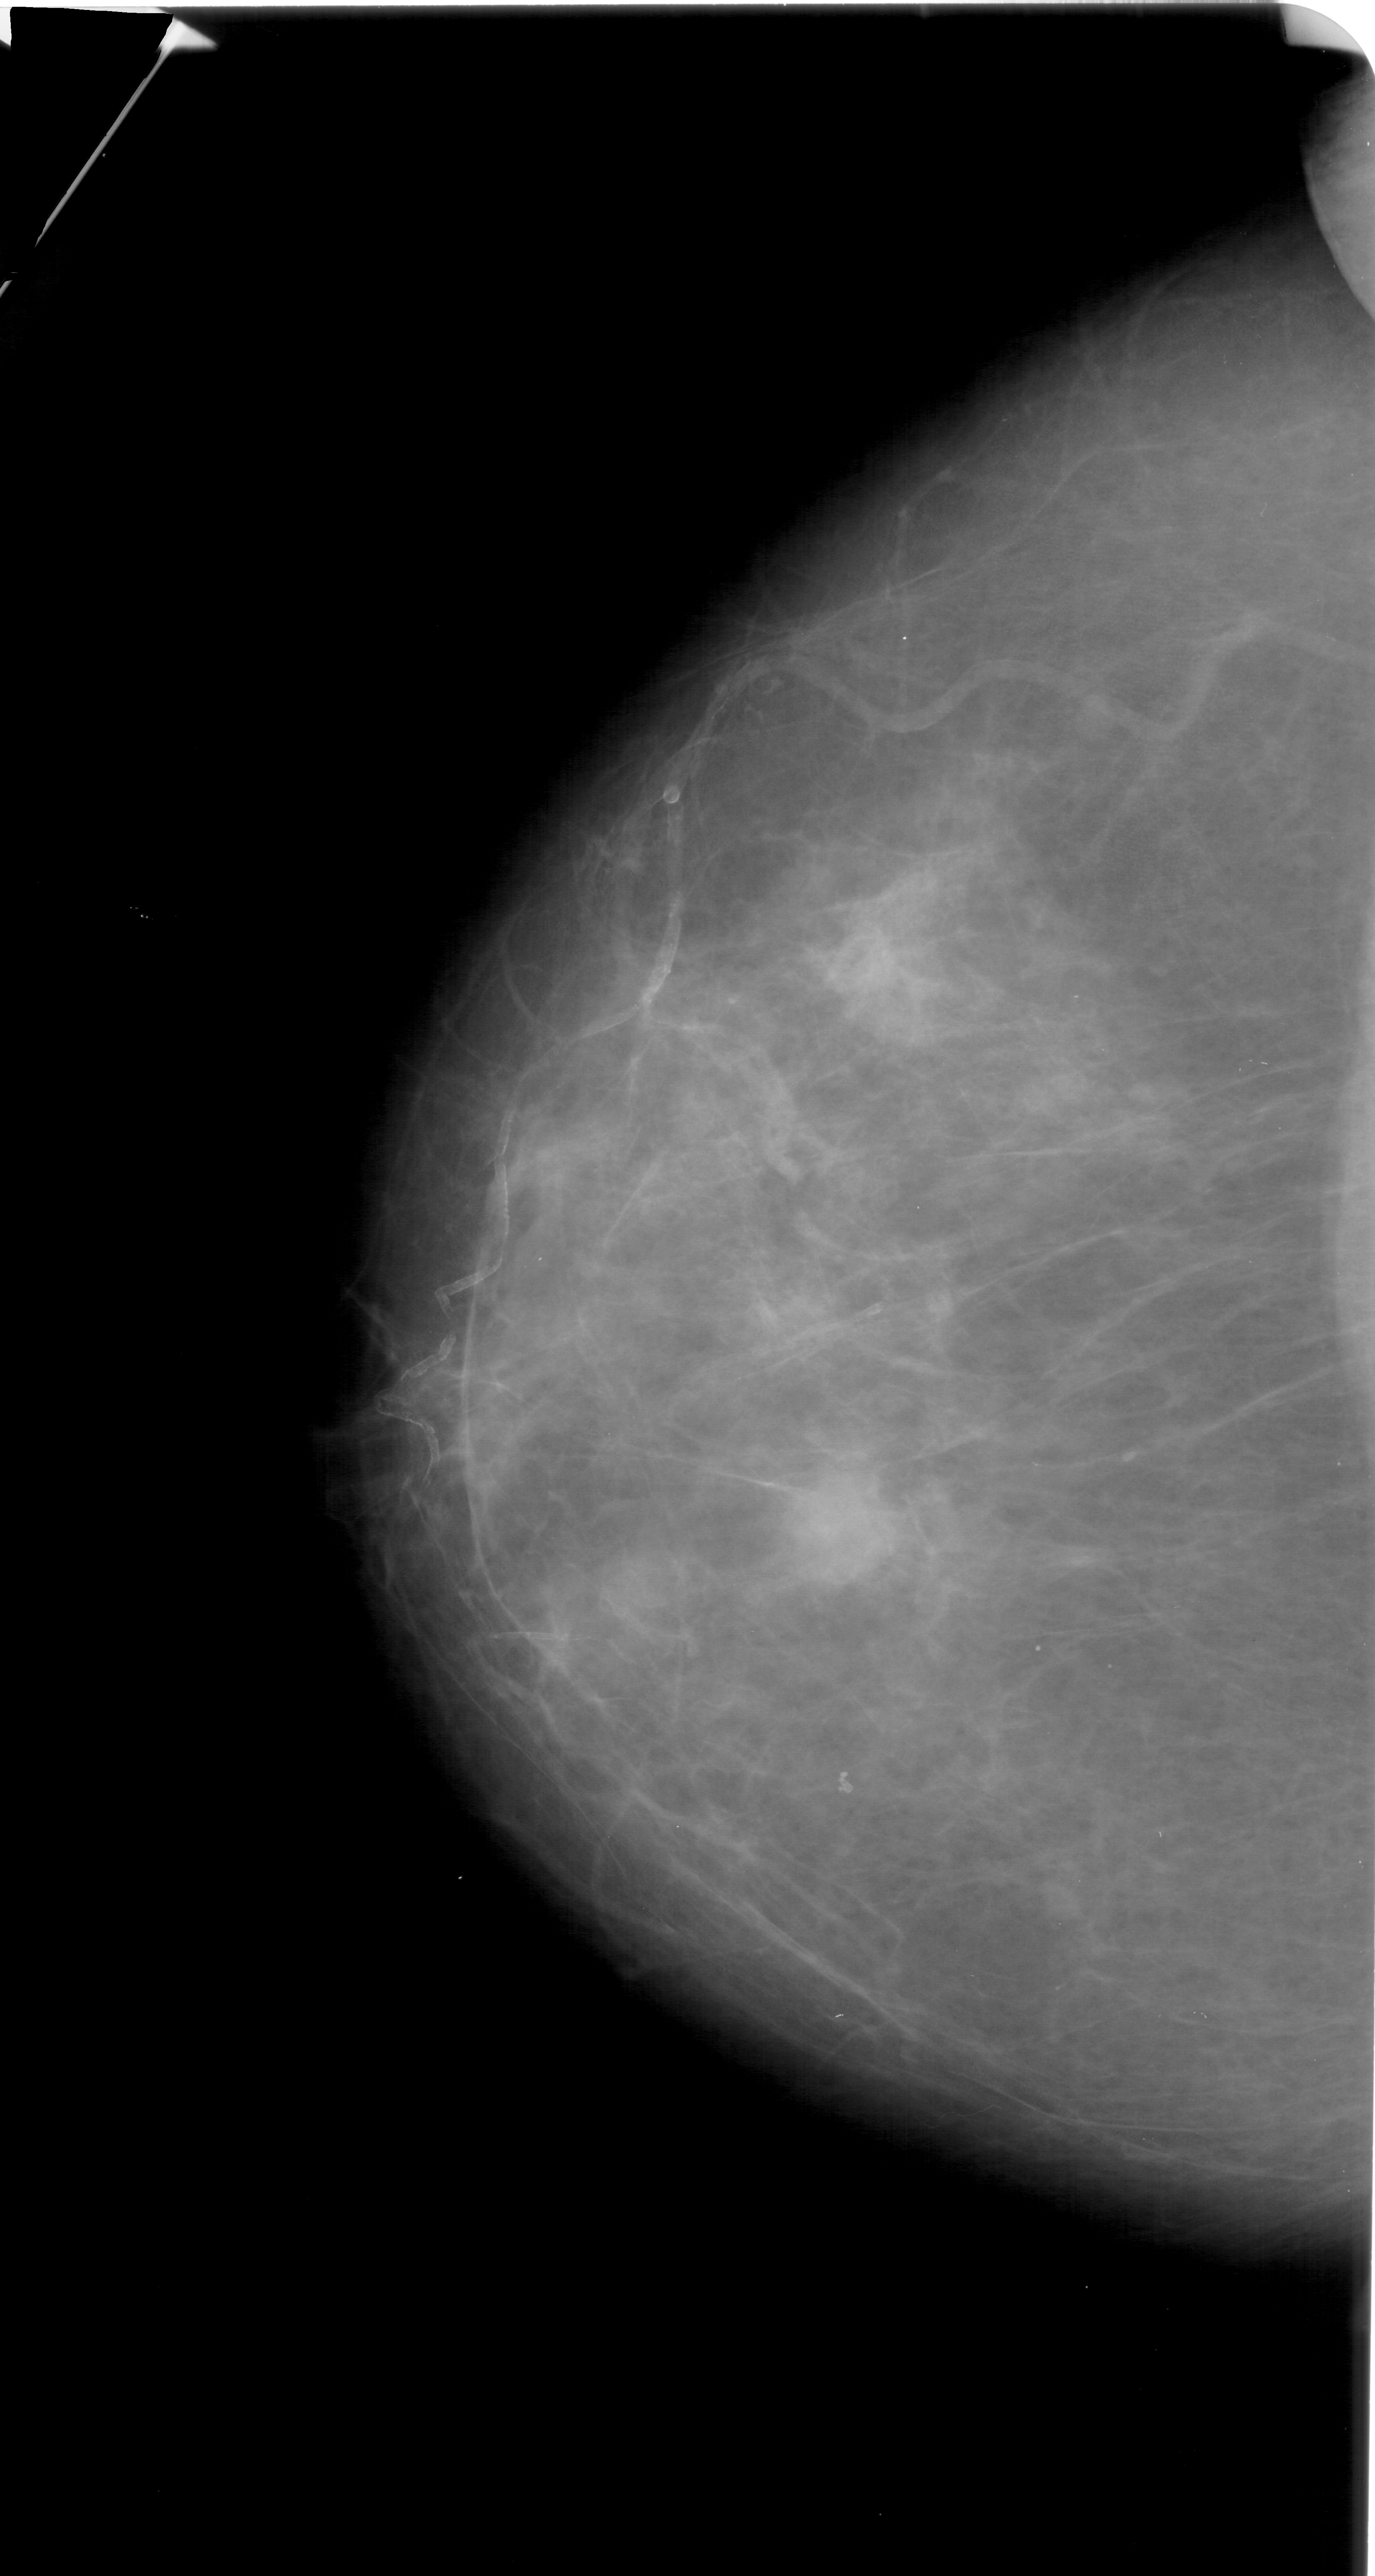
Mammogram (digitized film), left breast, CC view, BI-RADS breast density category 3 (scale 1–4).
Finding: mass, shape round, margins ill defined; BI-RADS assessment category 4; pathology result (as recorded, not read from the image): malignant.